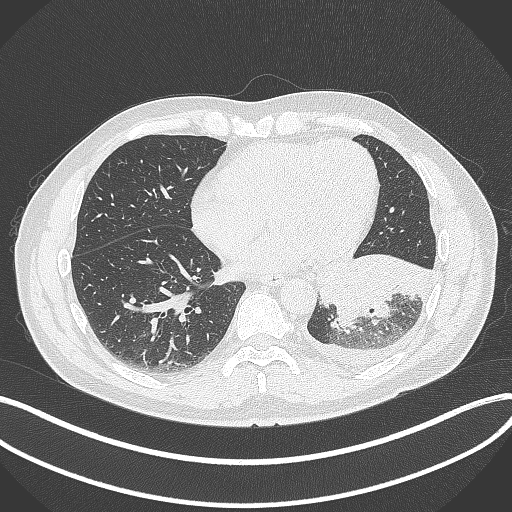
Chest CT, one axial slice. Slice 126 of 342 in the series (ordered by position). 120 kVp. Lung window (W 1500 / L -600 HU). 512 × 512 image matrix, field of view 400 × 400 mm. Patient: male, 58 years. Case-level facts recorded for this patient, not image findings: clinical TNM (as recorded): T3 N1 M1b; histopathological grade: G3.
Structures marked on this image (bounding box drawn by a radiologist):
- lung tumour (recorded histology: small cell carcinoma): bounding box <318,249,436,332> (left, top, right, bottom; pixels)